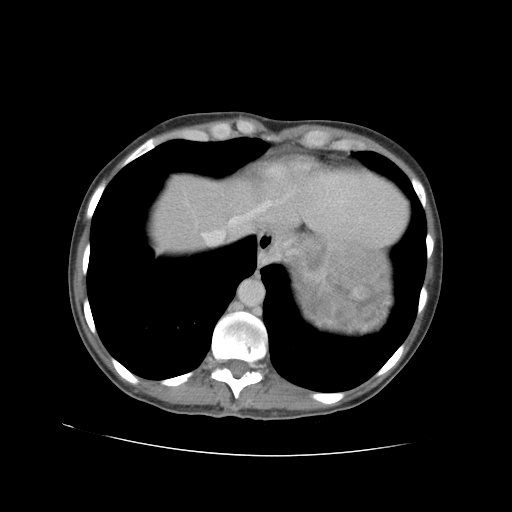
Contrast-enhanced abdominal CT, one axial slice; slice 81 of 90 in the series (ordered by position); intravenous contrast given; soft-tissue window (W 400 / L 40 HU); 512 × 512 image matrix, field of view 360 × 360 mm. Female patient. From the clinical record (not read from this slice): diagnosis: adrenocortical carcinoma; tumour side: left adrenal; tumour size at pathology: 18 cm; Ki-67 index: 11 %; stage (as recorded): 3.
Annotated regions visible in this slice (semi-automatic segmentation, software-assisted and operator-edited):
- mass: bounding box [x1, y1, x2, y2] px = [287, 237, 389, 329]